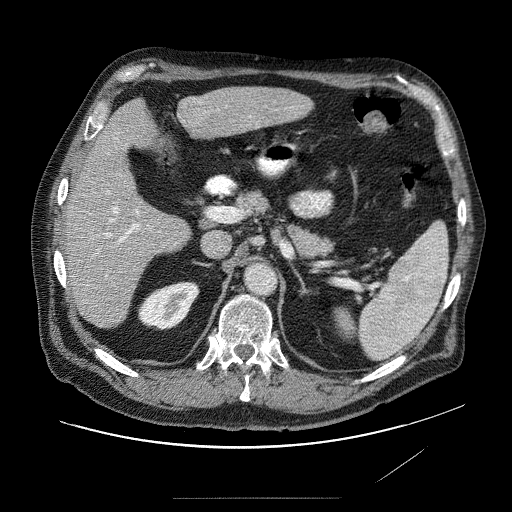
Contrast-enhanced abdominal CT (liver protocol), one axial slice. Slice 39 of 89 in the series (ordered by position). Reconstruction kernel STANDARD. 120 kVp. Soft-tissue window (W 400 / L 40 HU). 2.5 mm slice thickness. 512 × 512 image matrix, field of view 420 × 420 mm. From the clinical record (not read from this slice): diagnosis: hepatocellular carcinoma (patient treated with transarterial chemoembolisation; whether this scan precedes or follows treatment is not stated here); TNM stage (as recorded): Stage-IVA; Child-Pugh class: A; tumour differentiation: moderately differentiated.
Structures marked on this image (semi-automatically segmented with operator editing):
- liver parenchyma outside the tumour (the mass and vessels are separate outlines, so this box may not span the whole liver): bounding box (x1, y1, x2, y2) in pixels: (60, 84, 318, 330)
- mass: (183, 98, 211, 123)
- liver vessels: (91, 105, 235, 309)